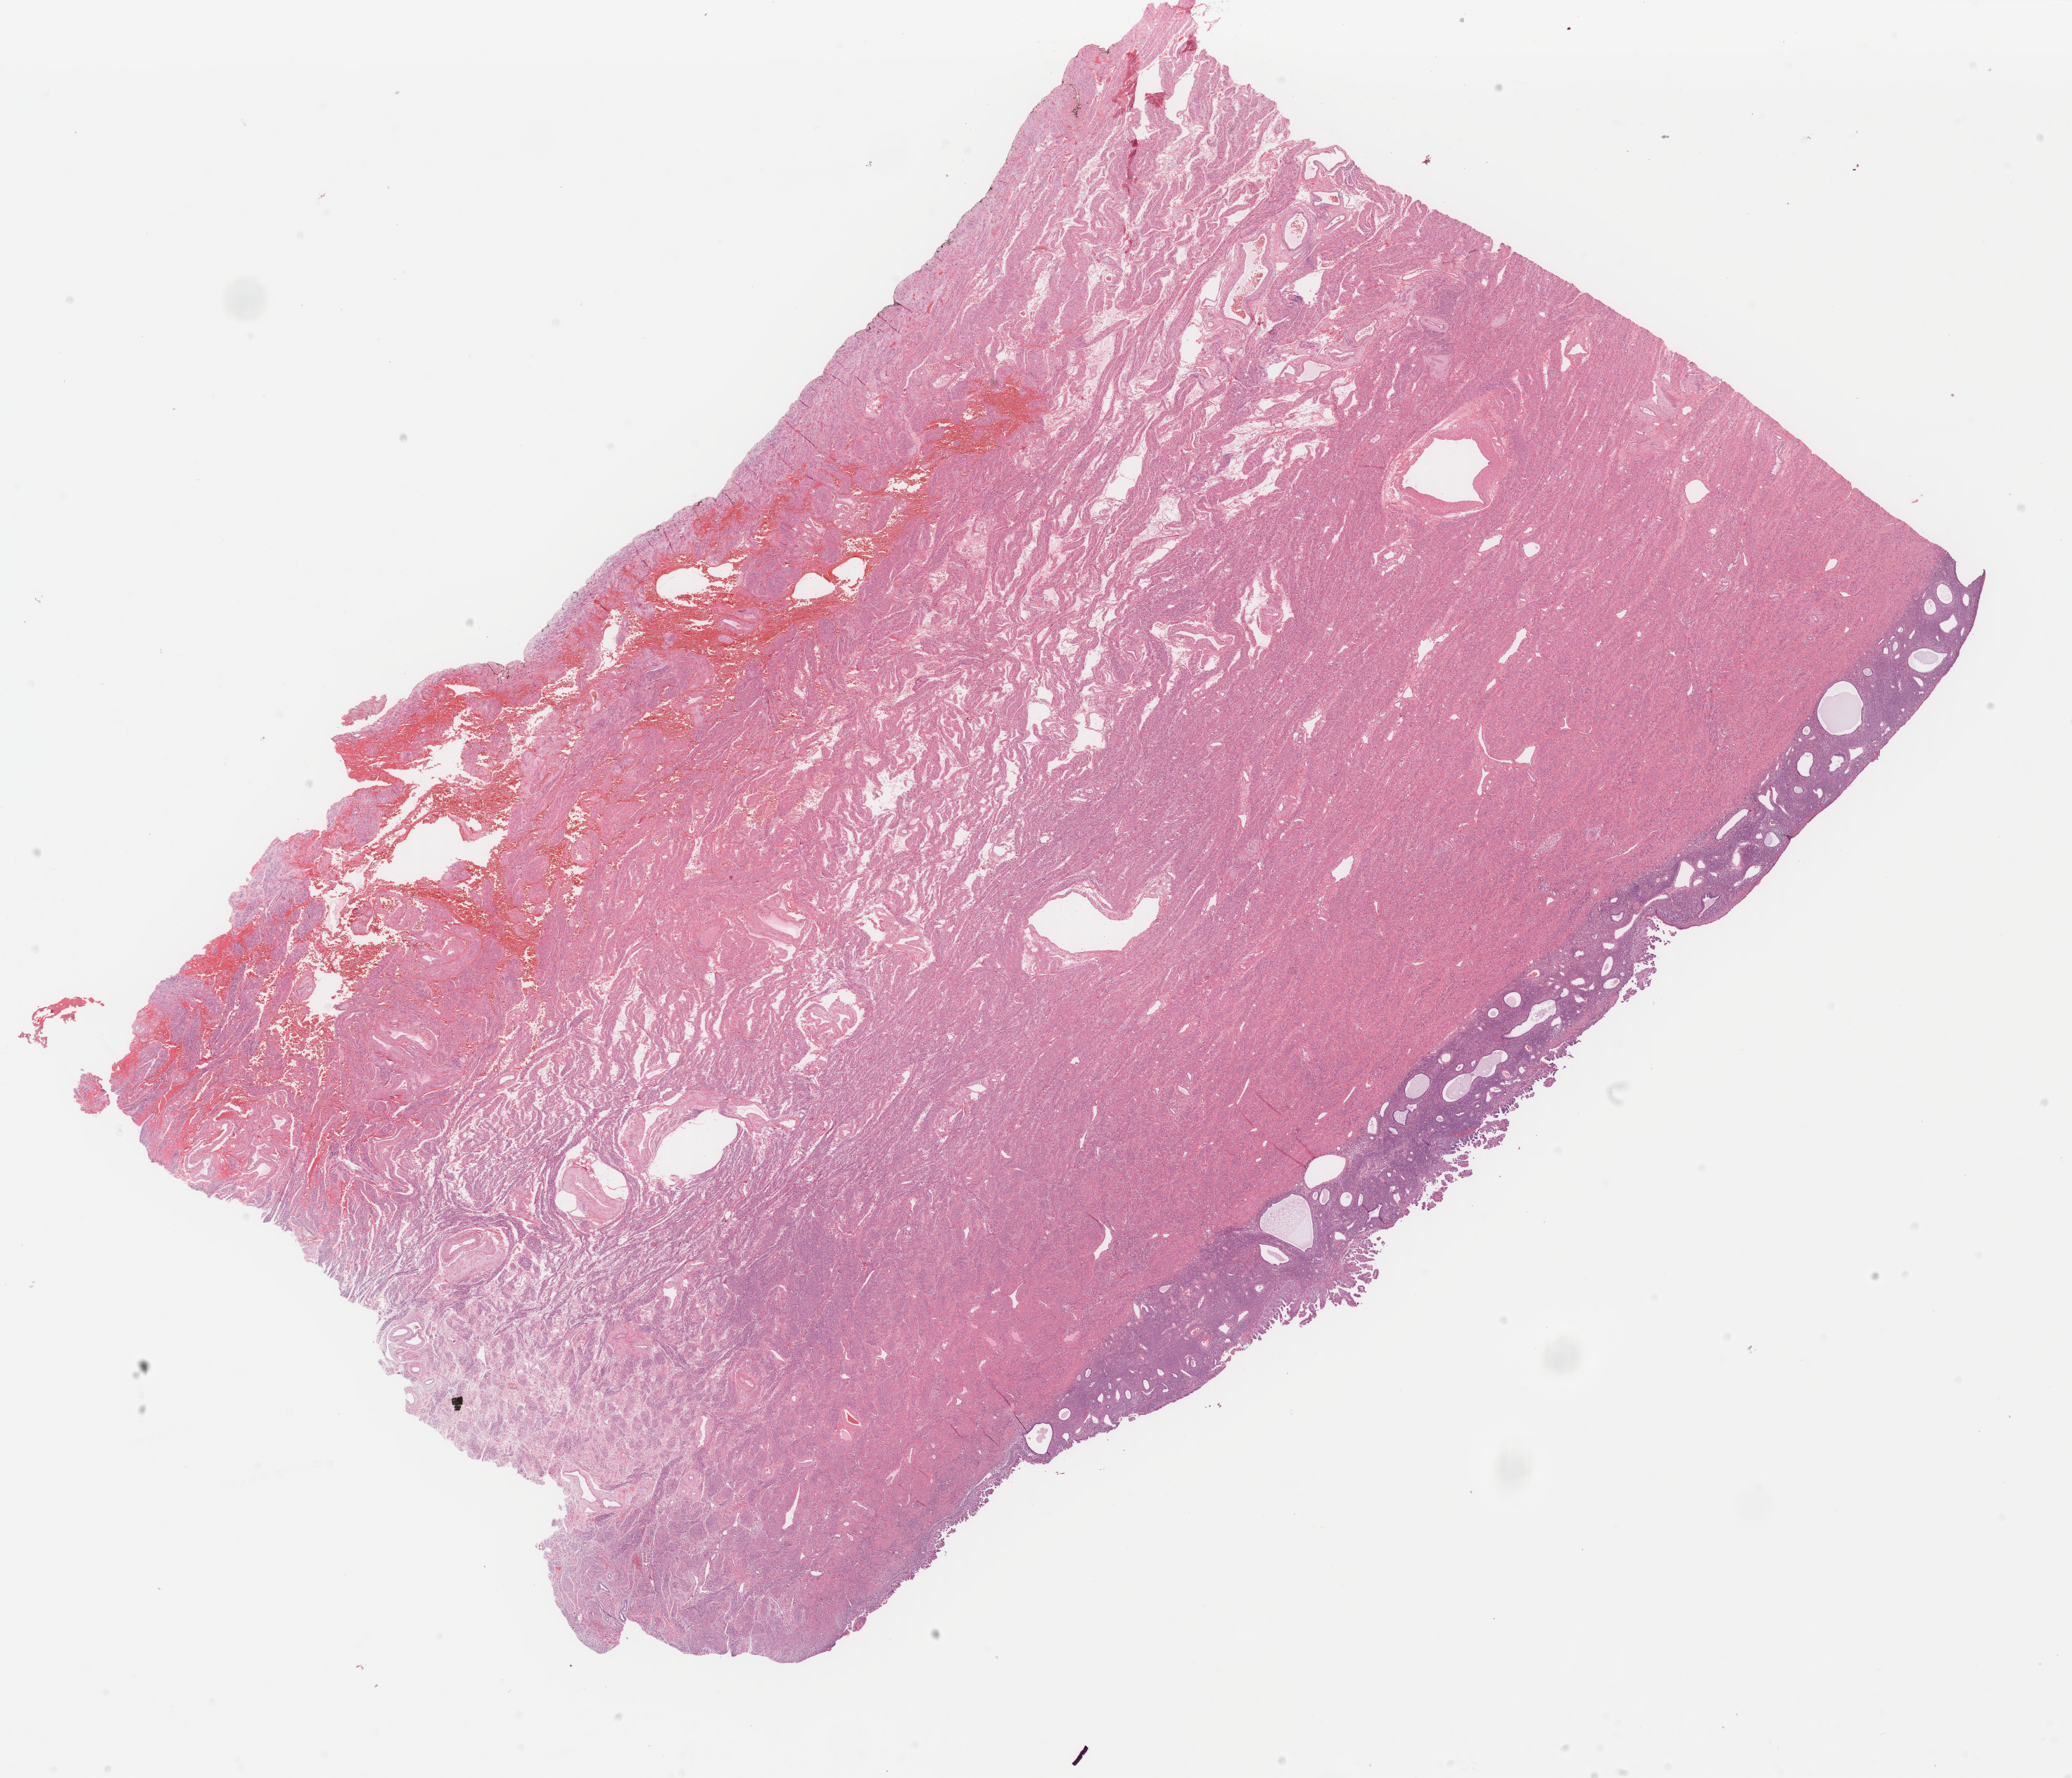
H&E whole-slide image, low-resolution overview of the scanned area, about 23.4 x 20.1 mm. Formalin-fixed paraffin-embedded (FFPE) diagnostic section. Sample: primary tumour, uterus. Female, age 76 years at initial diagnosis. Histologic grade: G3 (poorly differentiated).
Histologic diagnosis: Serous cystadenocarcinoma, NOS (endometrium). FIGO stage: IA.